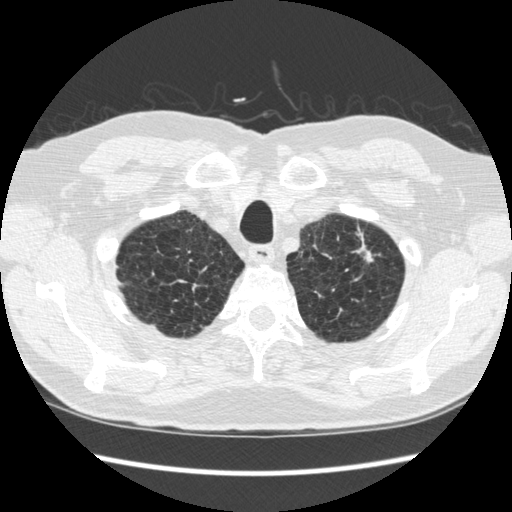
Axial slice from a low-dose chest CT screening exam, second annual screen, lung window (W 1500 / L -600 HU), 1.25 mm slice thickness, 120 kVp. Male participant, aged 70 years at enrolment.
Expert reader's lesion annotation, bounding box <328,226,390,294> (left, top, right, bottom; pixels). The screening reader recorded 5 non-calcified nodules or masses ≥4 mm on this exam (right lower lobe, right lower lobe, right lower lobe, left upper lobe, left lower lobe); which of them this box marks is not recorded. Participant outcome: lung cancer diagnosed 479 days after this screen — squamous cell carcinoma, NOS, left upper lobe, moderately differentiated (G2), stage IA (AJCC 6th edition), 18 mm at pathology.